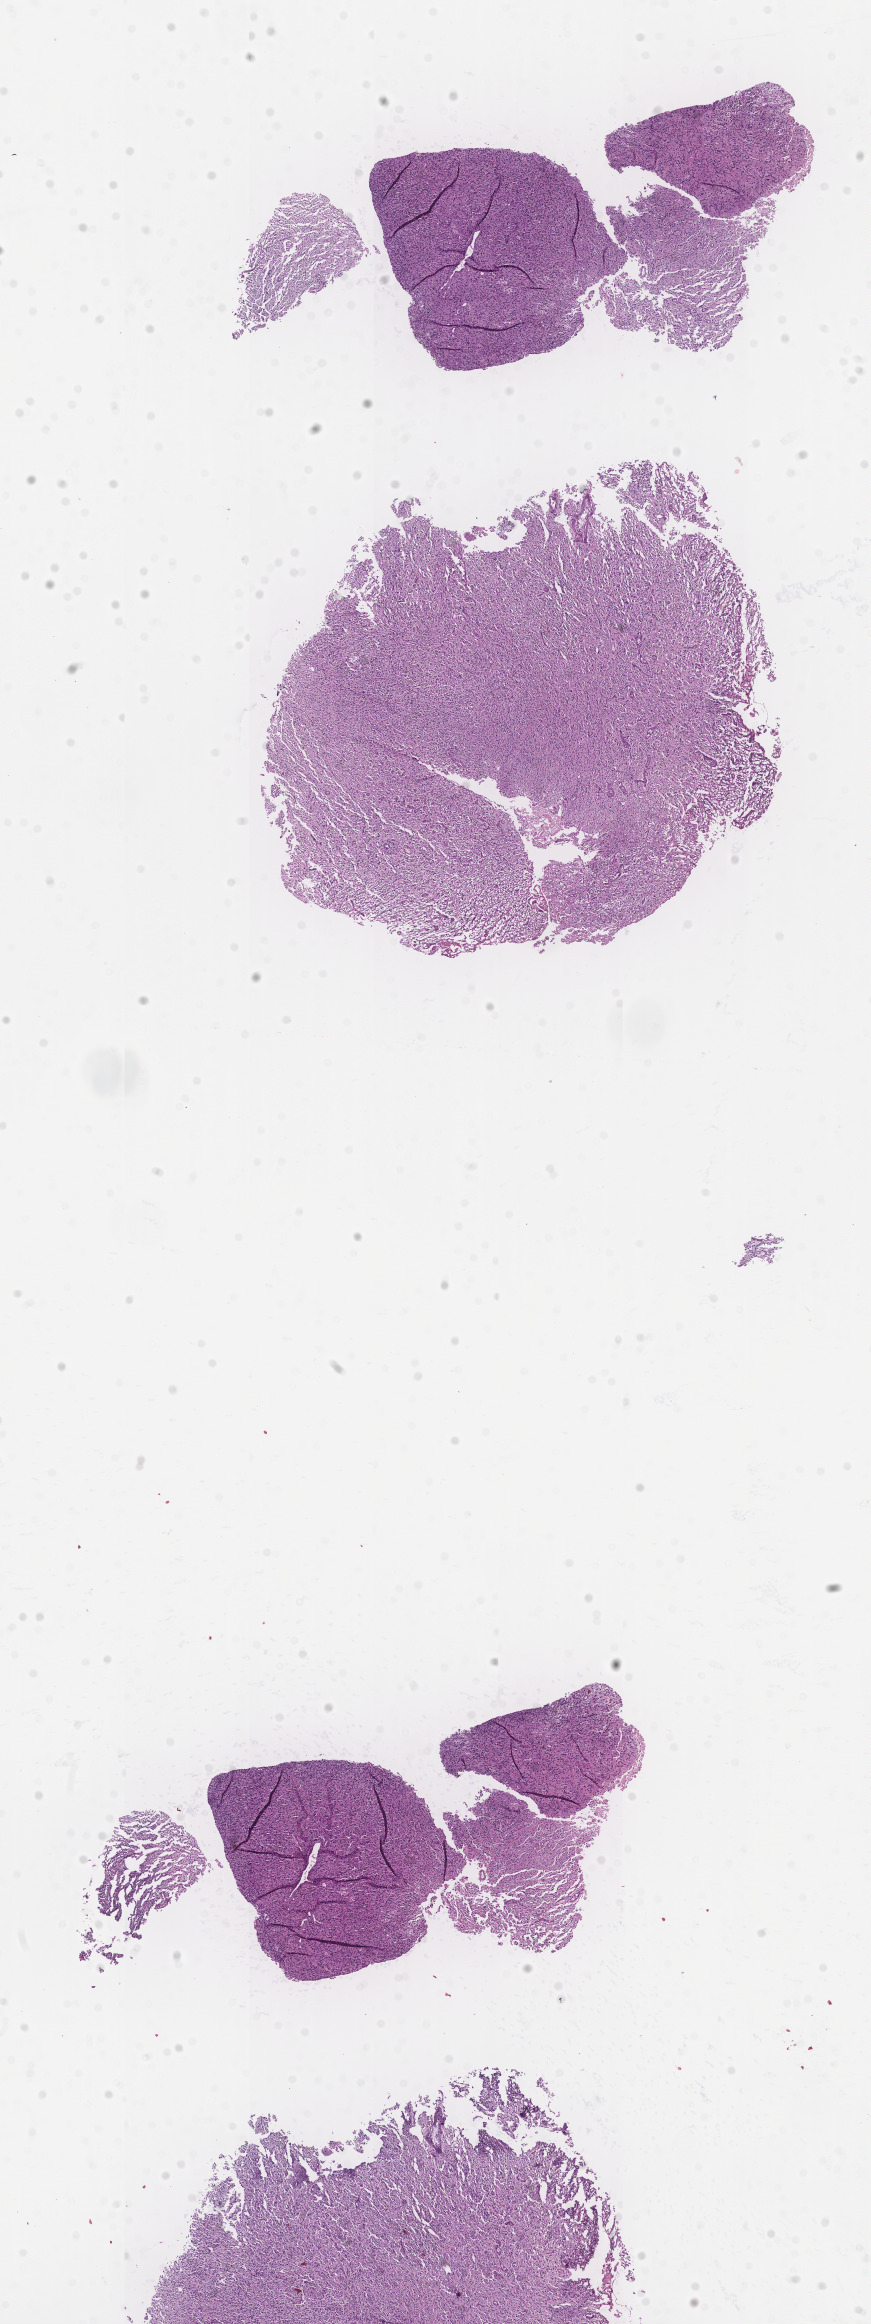
Whole-slide histology image, H&E-stained, shown as a low-resolution overview of the whole scanned area (about 7.0 x 18.7 mm, slide scanned at 20x). Tumour tissue sample, sampled site: brain. 51-year-old female patient. Pathologist review of this section (percent, as recorded): tumour nuclei 80%, necrosis 5%.
Histologic diagnosis: Glioblastoma.